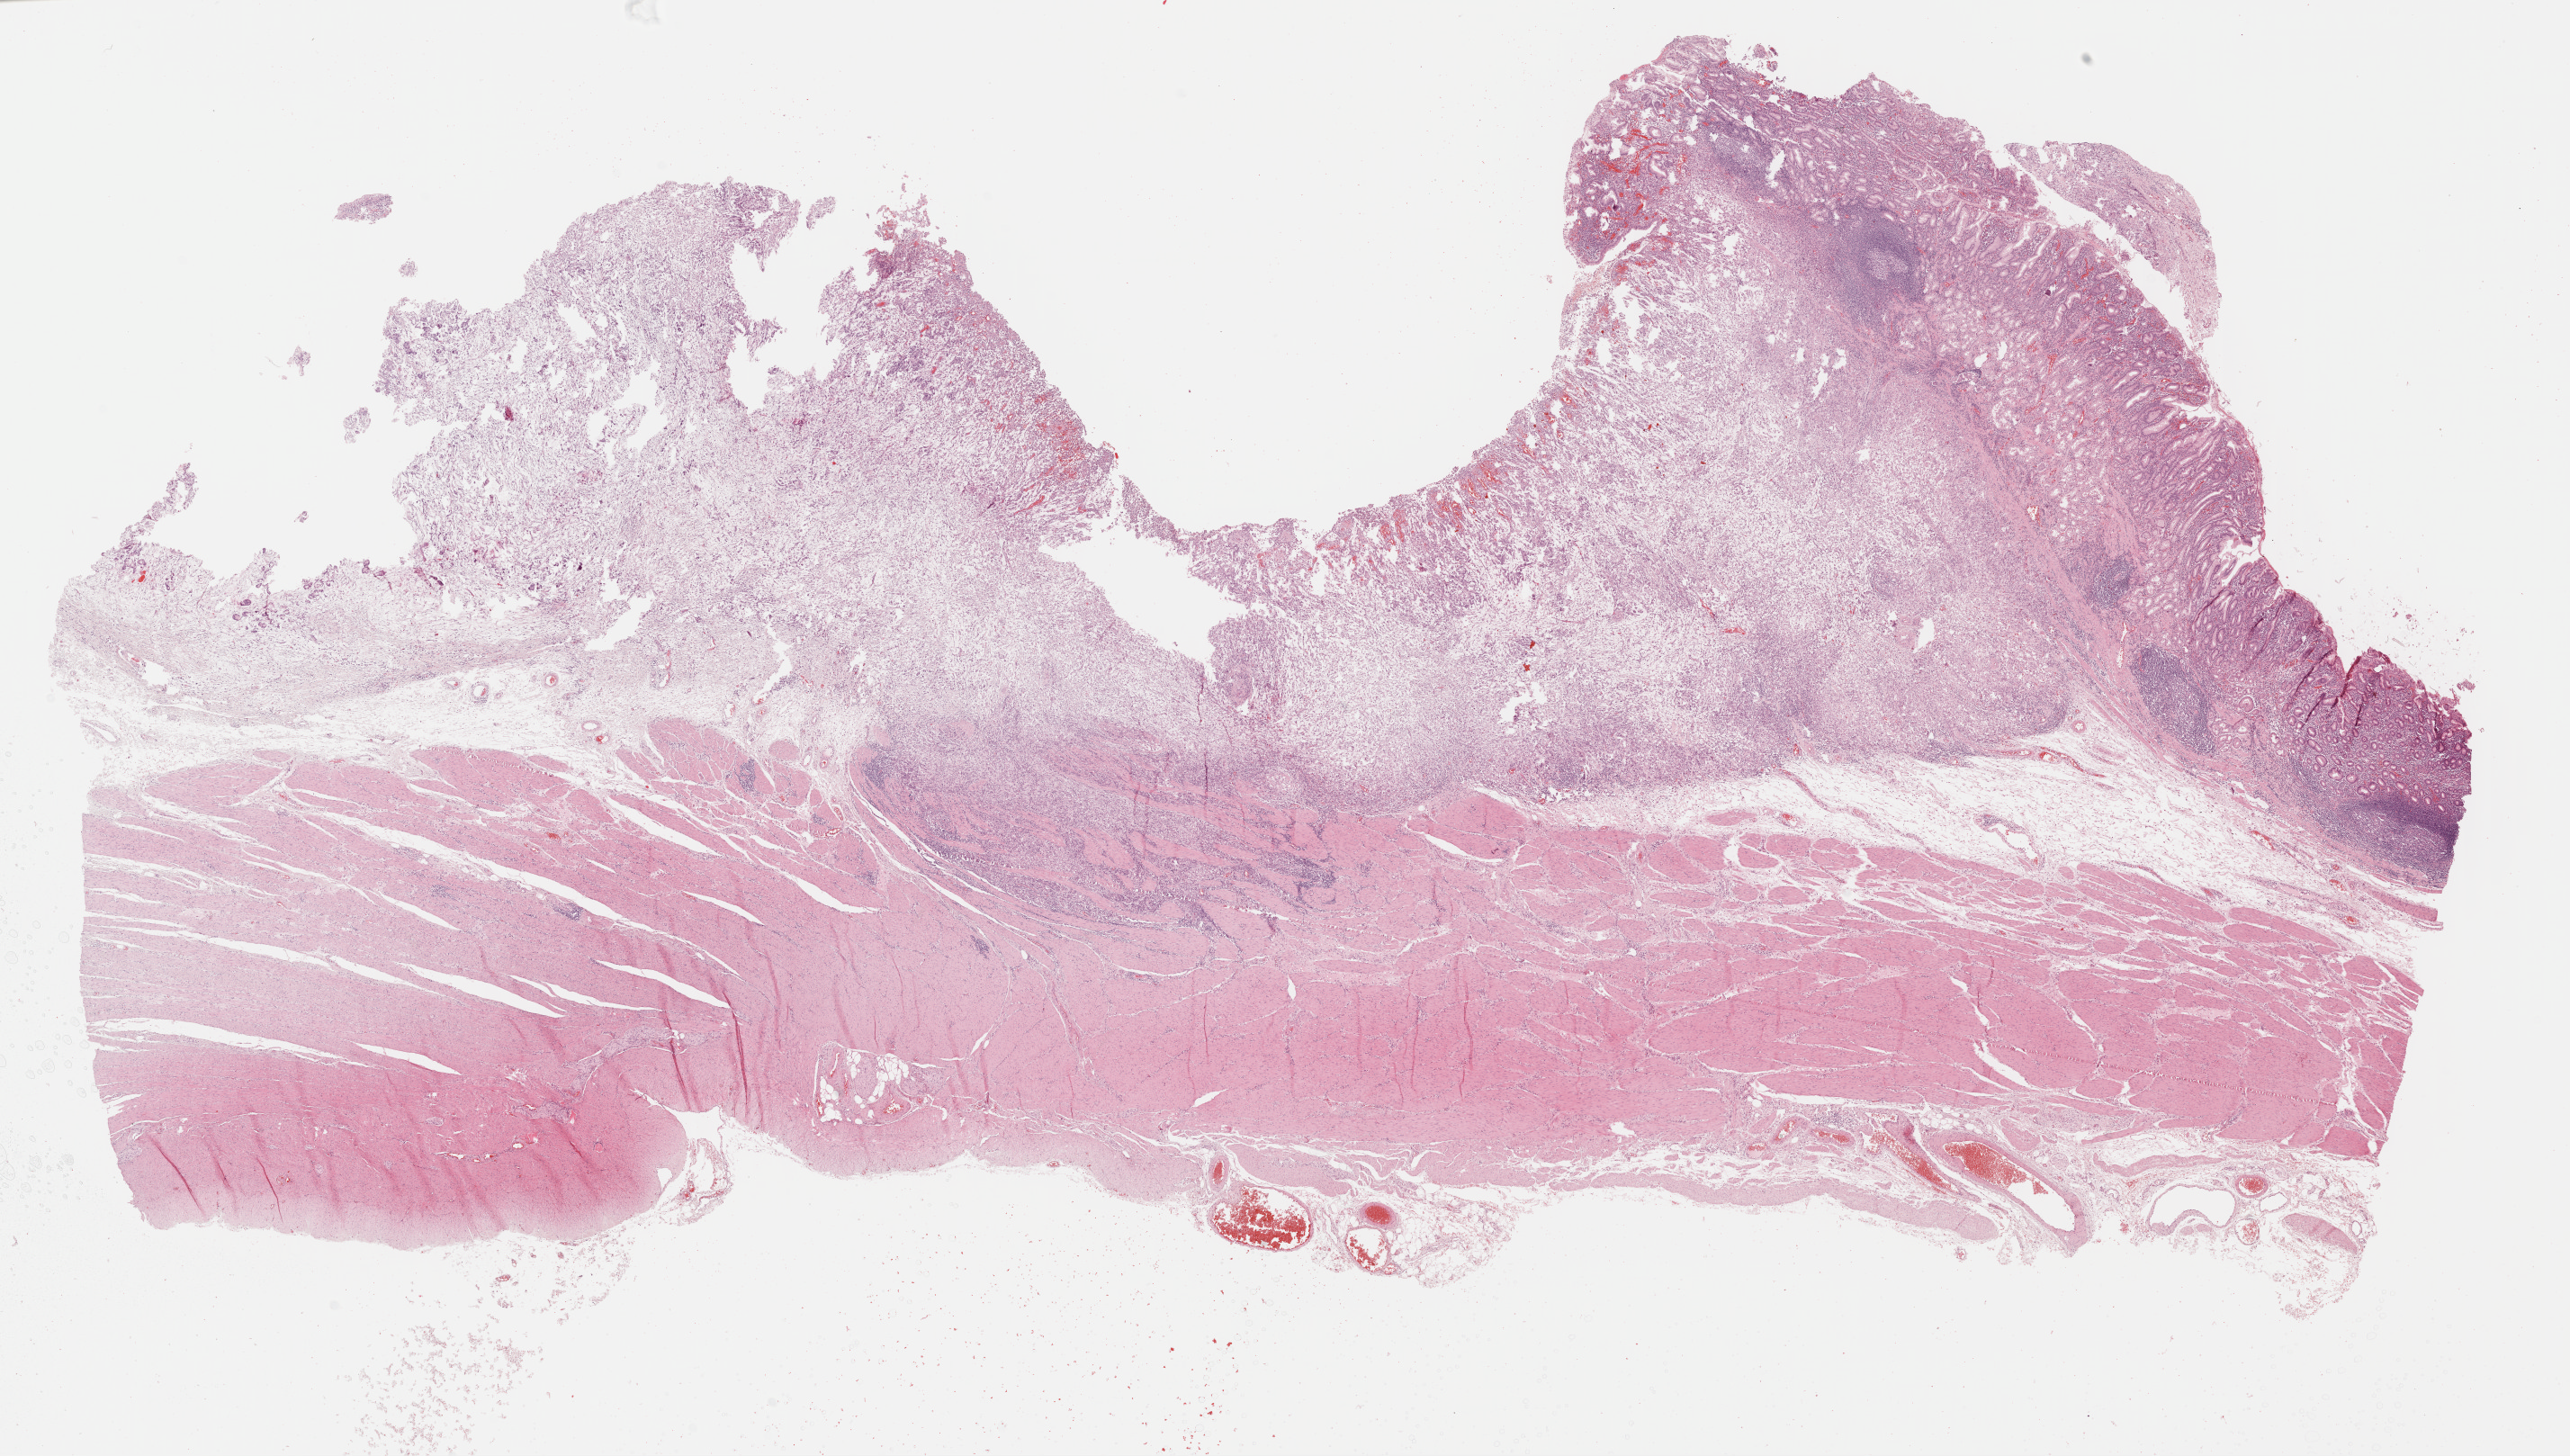
Whole-slide histology image, Hematoxylin and eosin (H&E) stained — a low-resolution overview of the entire scanned area, about 22.4 x 12.7 mm (acquisition: 40x scan); formalin-fixed paraffin-embedded (FFPE) diagnostic section; primary tumour sample from the stomach. Male patient; age at initial diagnosis 58 years. Histologic grade: G3 (poorly differentiated).
AJCC pathologic stage: IB. Diagnosis: Carcinoma, diffuse type (gastric antrum). Lymph nodes positive (case pathology): 0 of 11 examined.